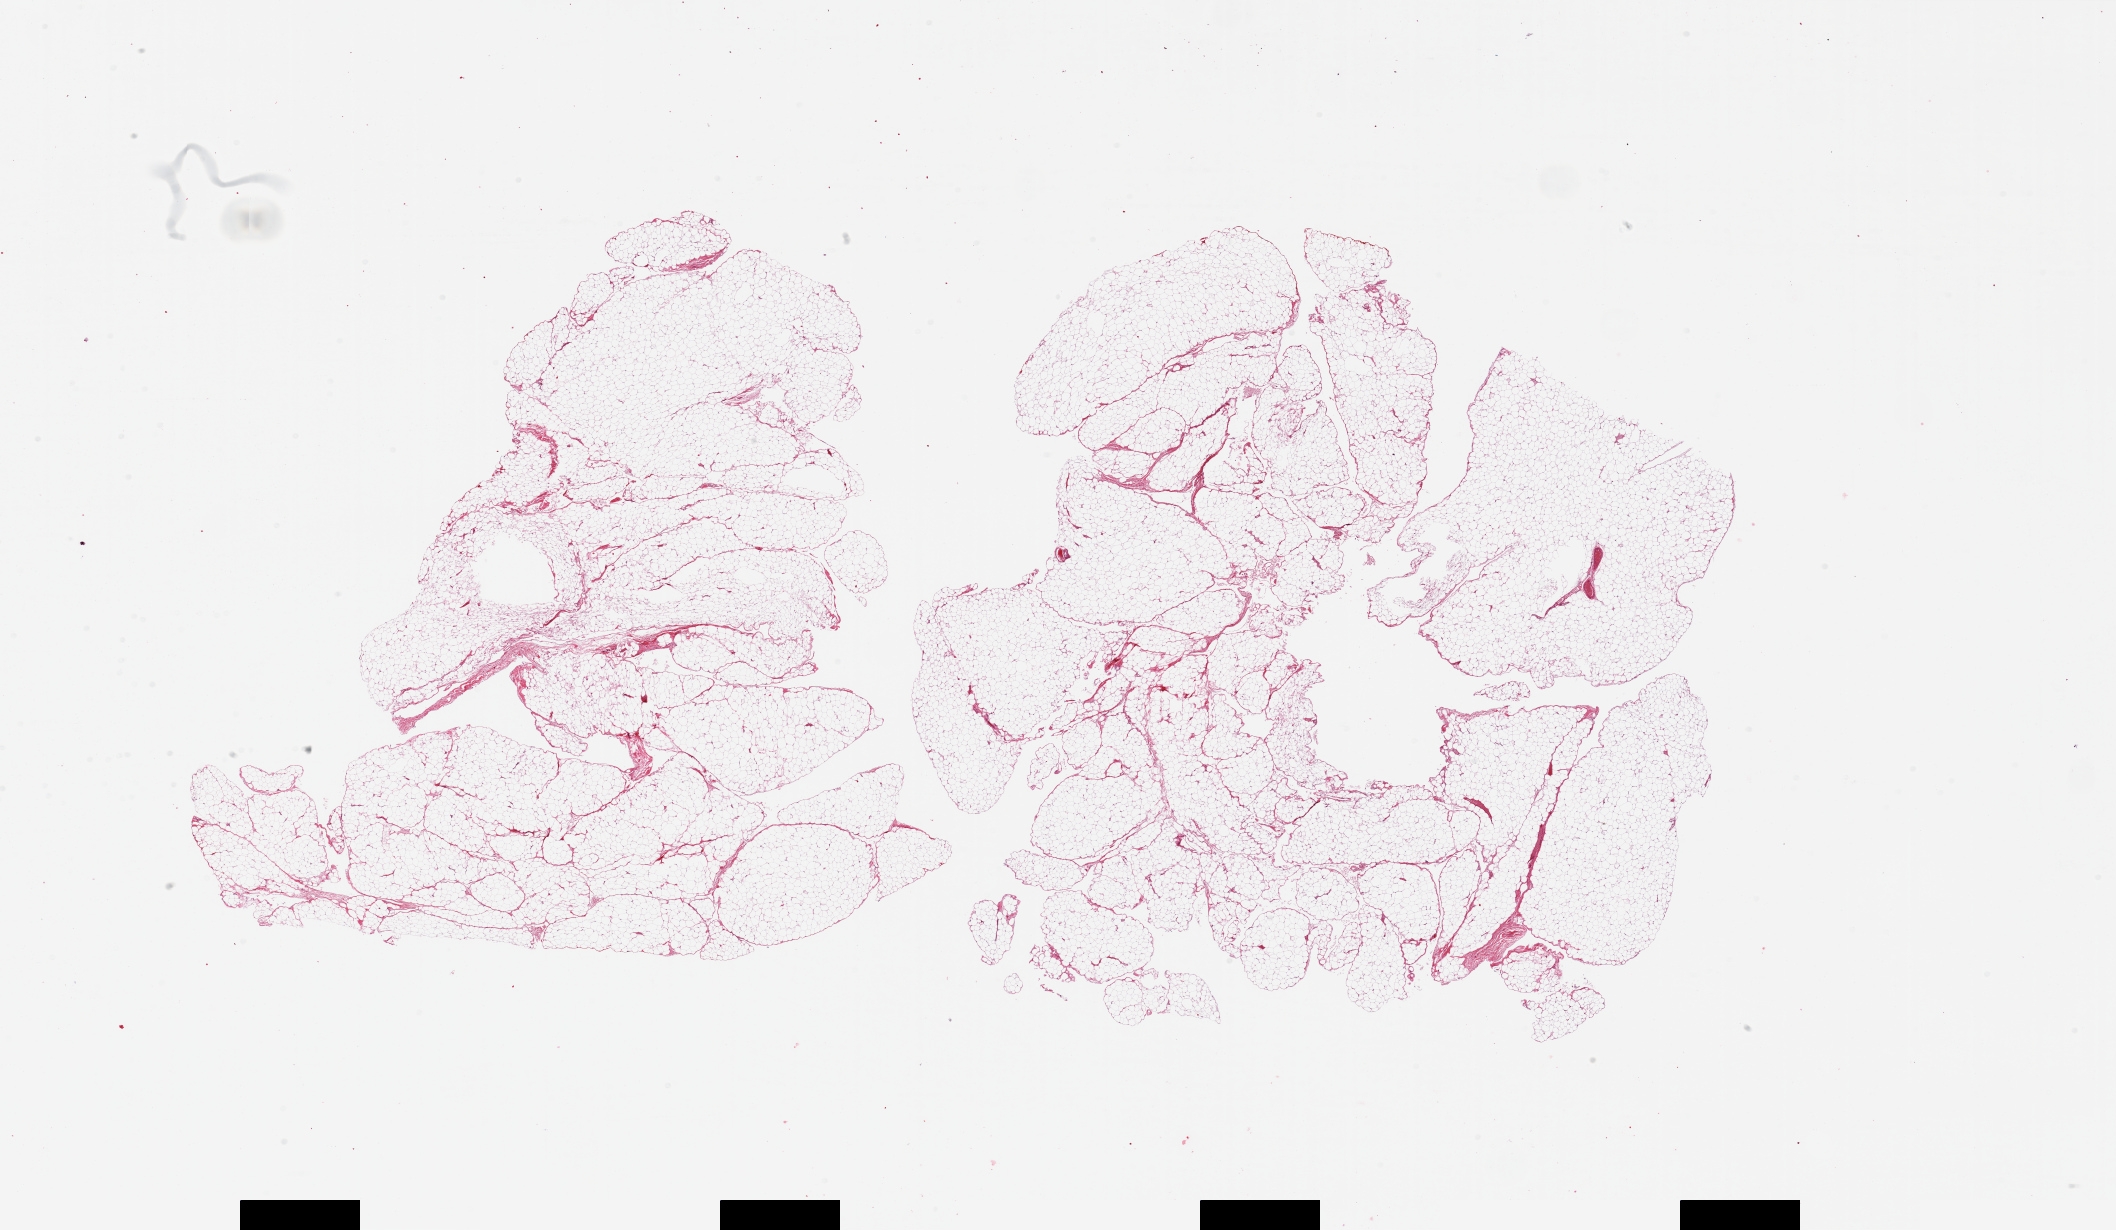
Digitized hematoxylin and eosin (H&E)-stained section, shown as a low-resolution overview of the whole scanned area (about 33.5 x 19.5 mm), PAXgene-fixed paraffin-embedded (PFPE) section, sampled site (target tissue): omentum, tissue donor sample.
Reviewer comment on this tissue sample: 2 pieces; fibrous content <2%.